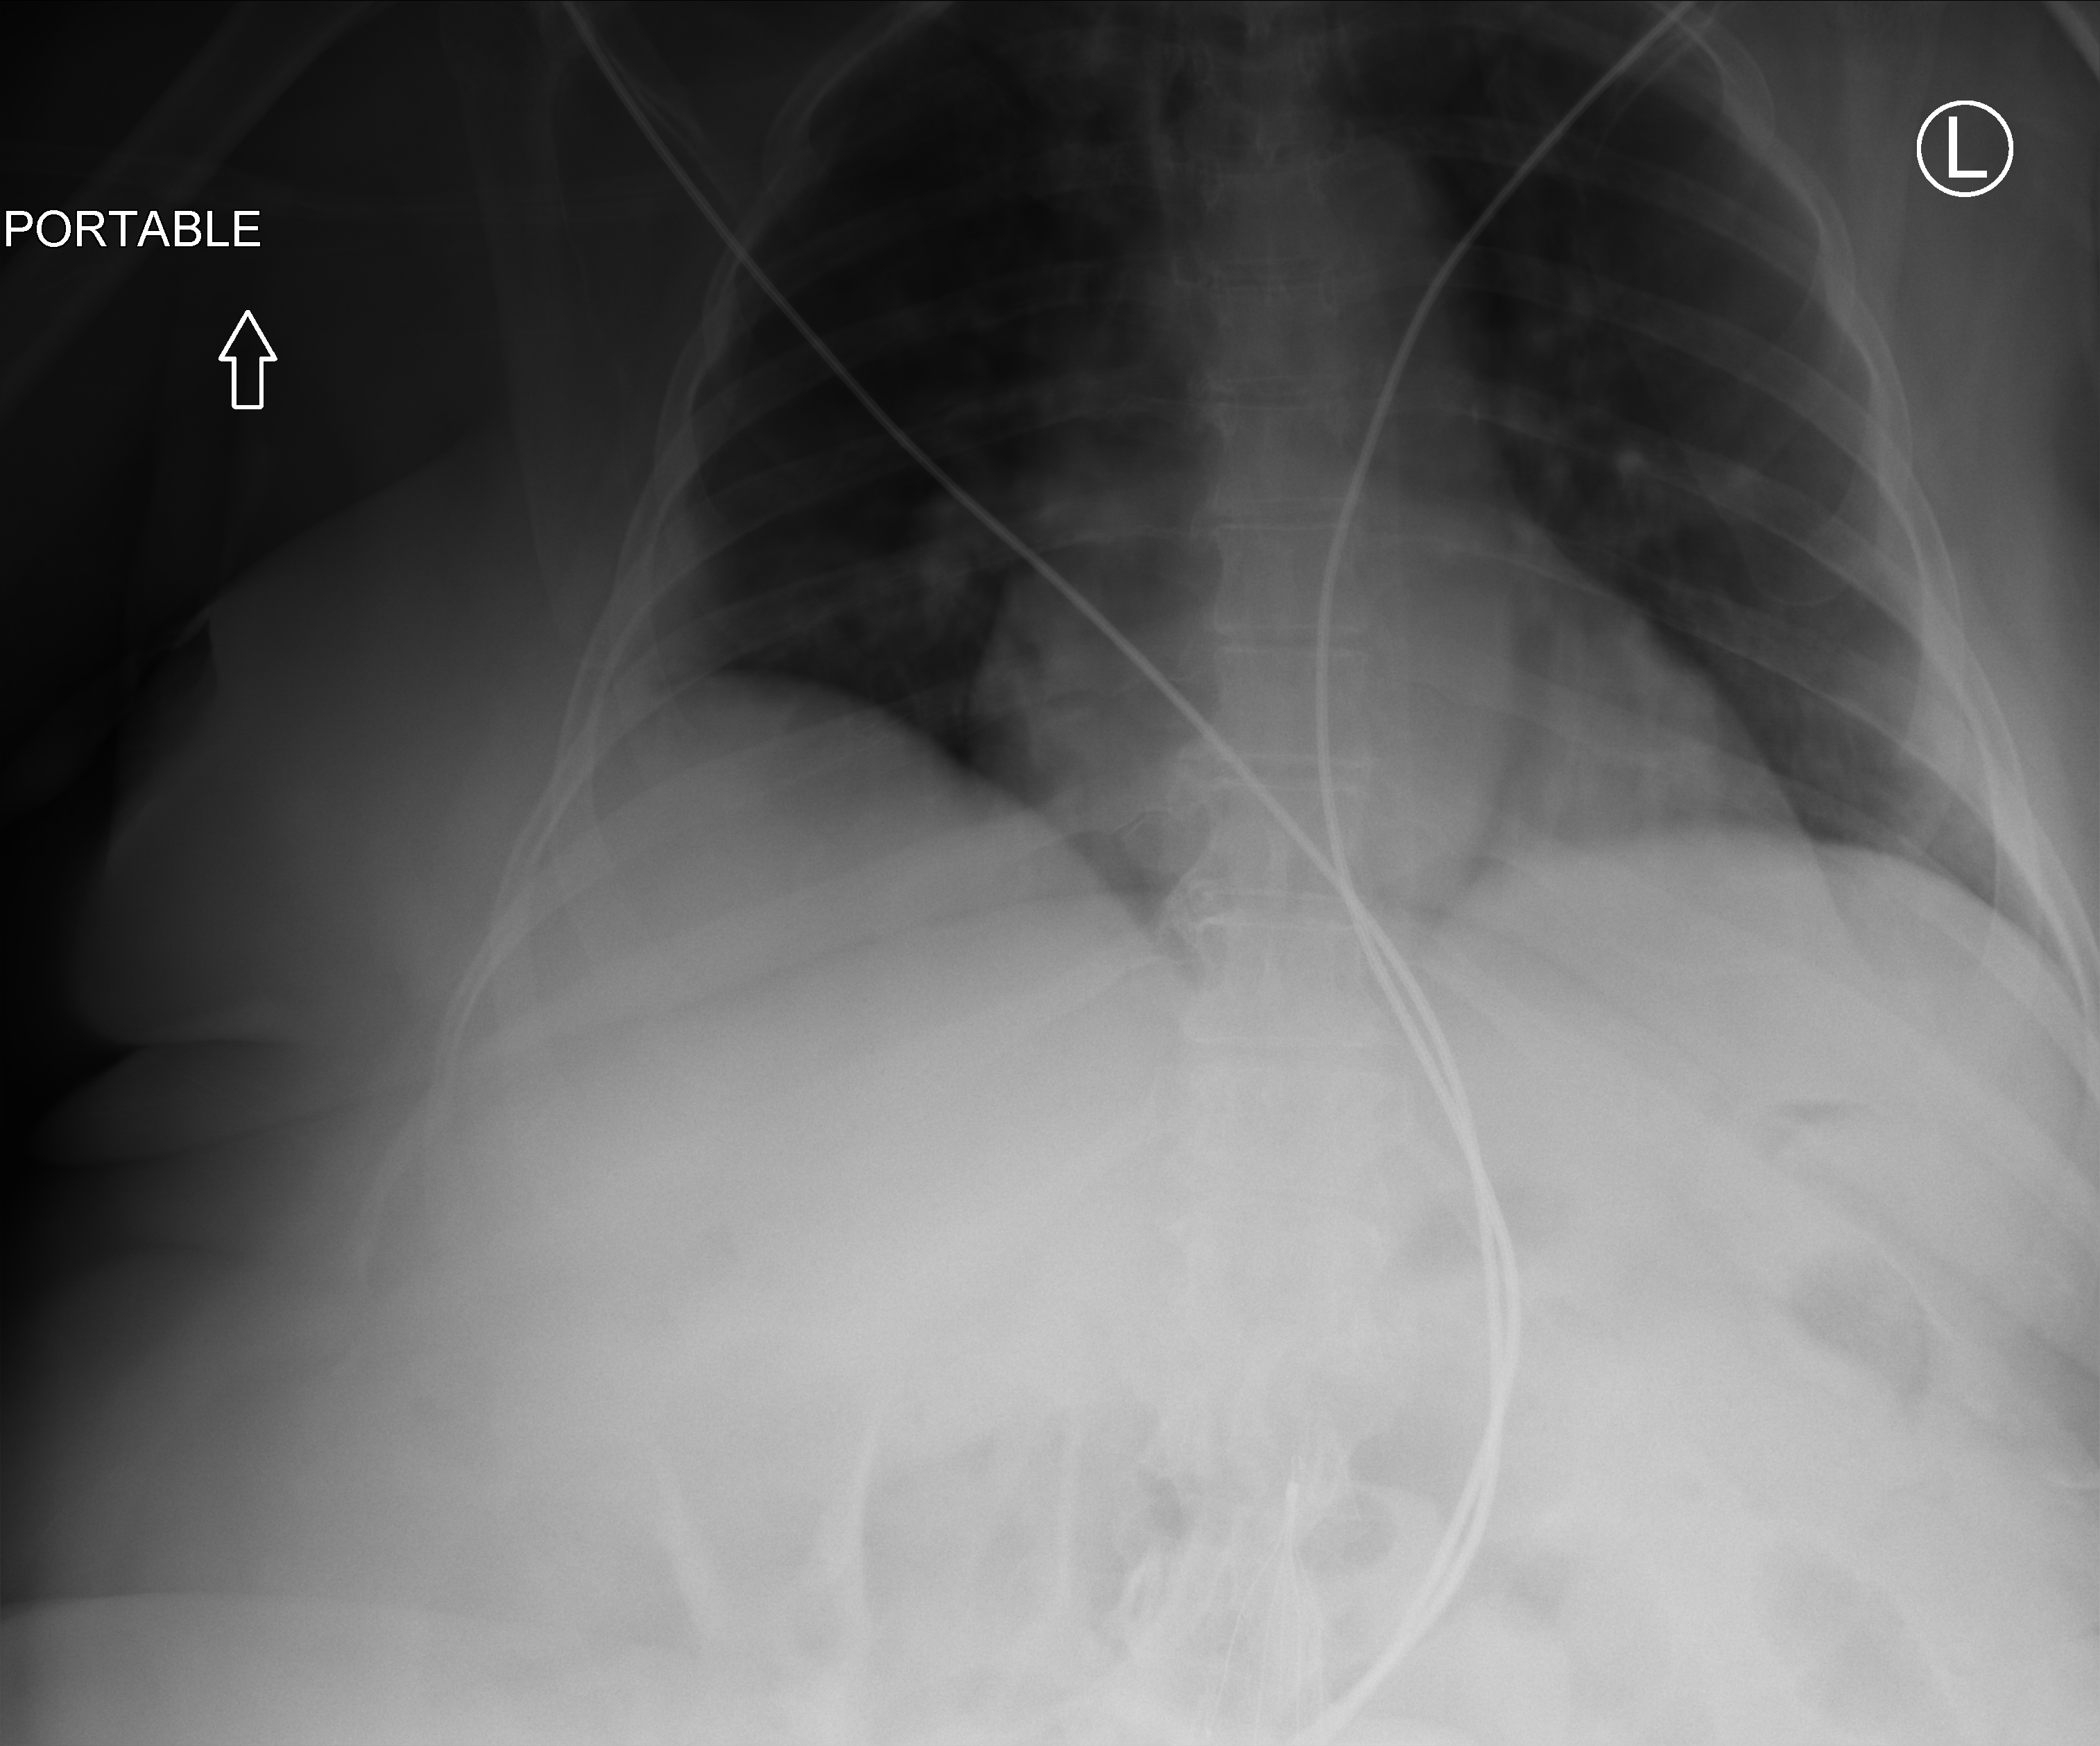
Portable abdomen radiograph, anteroposterior (AP) projection. Patient hospitalised with COVID-19; female, aged 60–74 years.
Admission-level facts for this patient (not findings on this image; timing relative to this image not recorded): admitted to intensive care during this hospital stay: no.